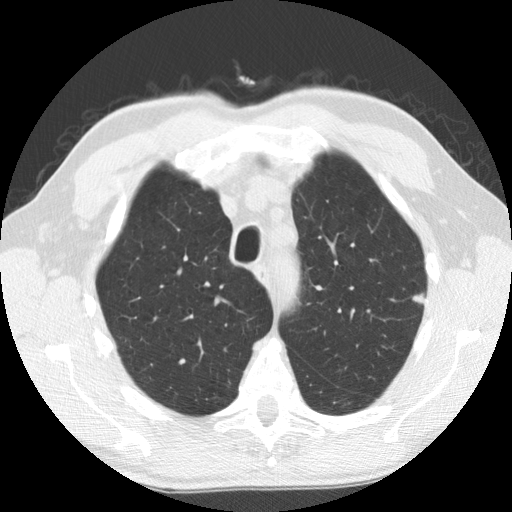
Low-dose screening chest CT, one axial slice. Position 130 of 158 along the scan axis. 120 kVp. Lung window (W 1500 / L -600 HU). 2.5 mm slice thickness. 512 × 512 image matrix, field of view 340 × 340 mm.
Outlined on this slice (expert manual segmentation):
- lesion 1 (tumor, upper lobe of left lung): bounding box [x1, y1, x2, y2] px = [412, 293, 427, 304]